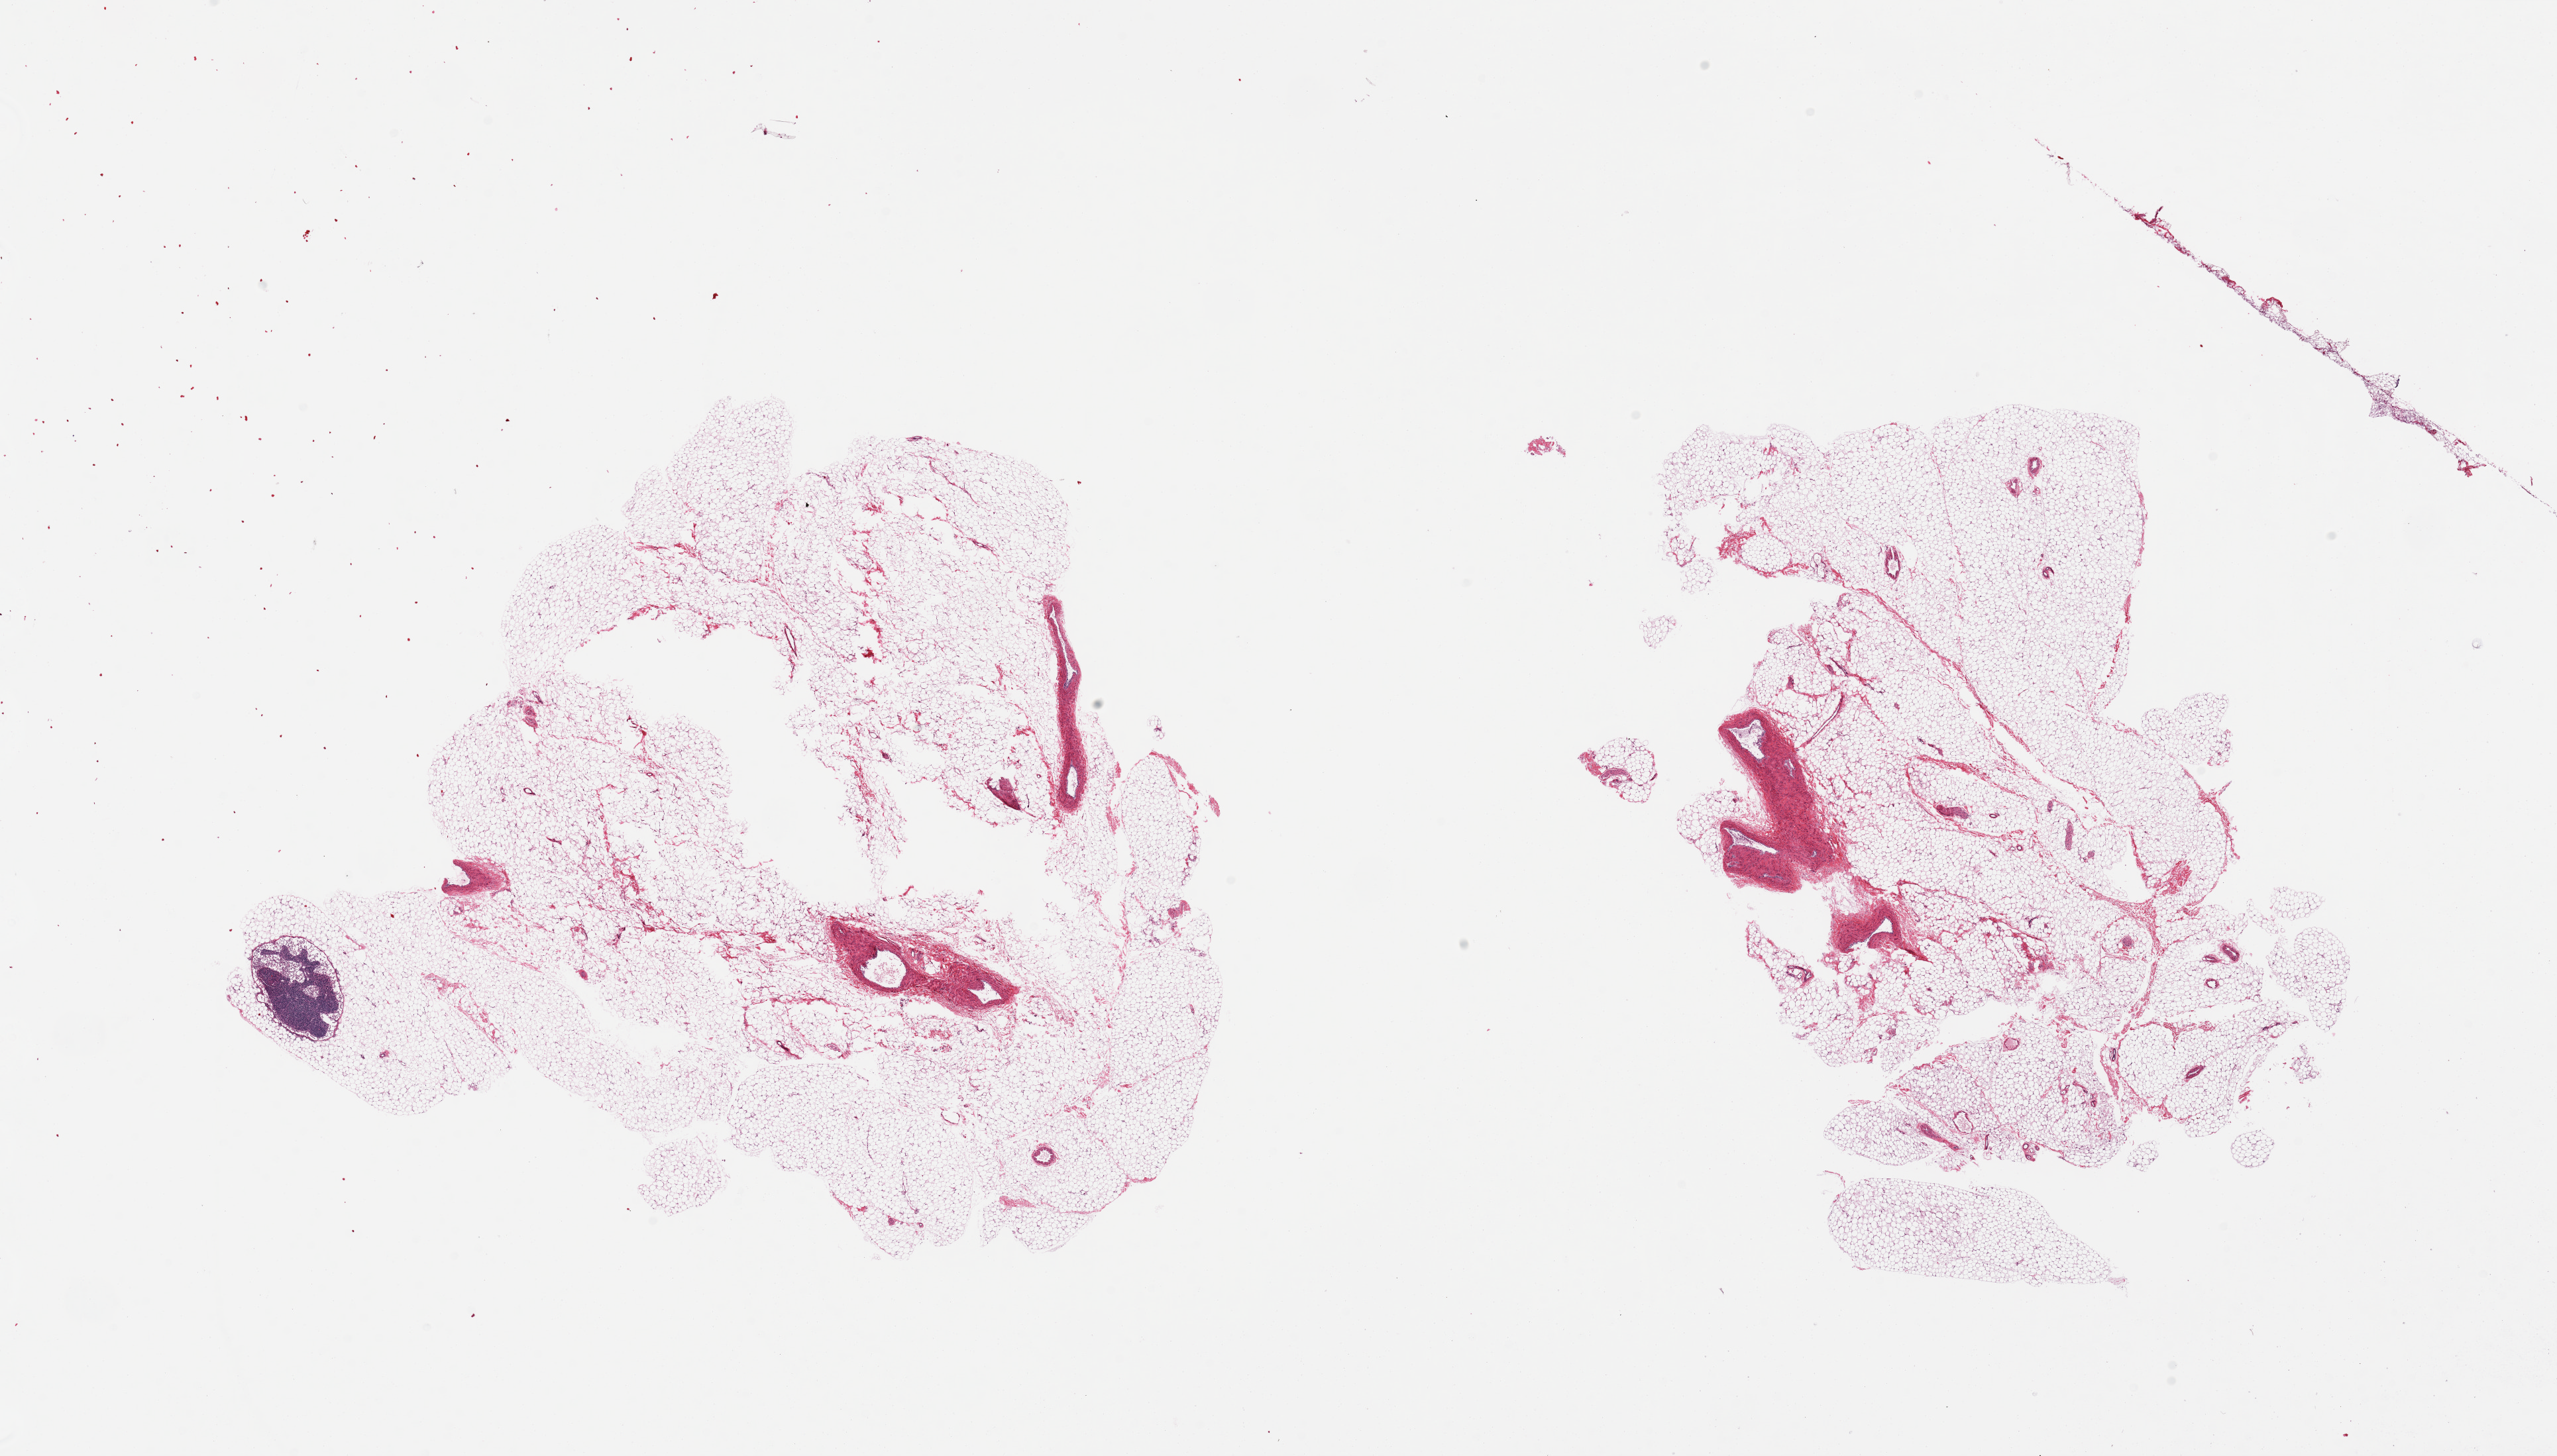
Whole-slide image, haematoxylin and eosin stain — whole scanned area (about 30.5 x 17.4 mm) shown as a low-resolution overview; PAXgene-fixed paraffin-embedded (PFPE) section; target tissue: omentum; tissue donor sample. Donor sex: male.
Reviewer comment on this tissue sample: 2 pieces, few larger vessels and incidental lymph node.